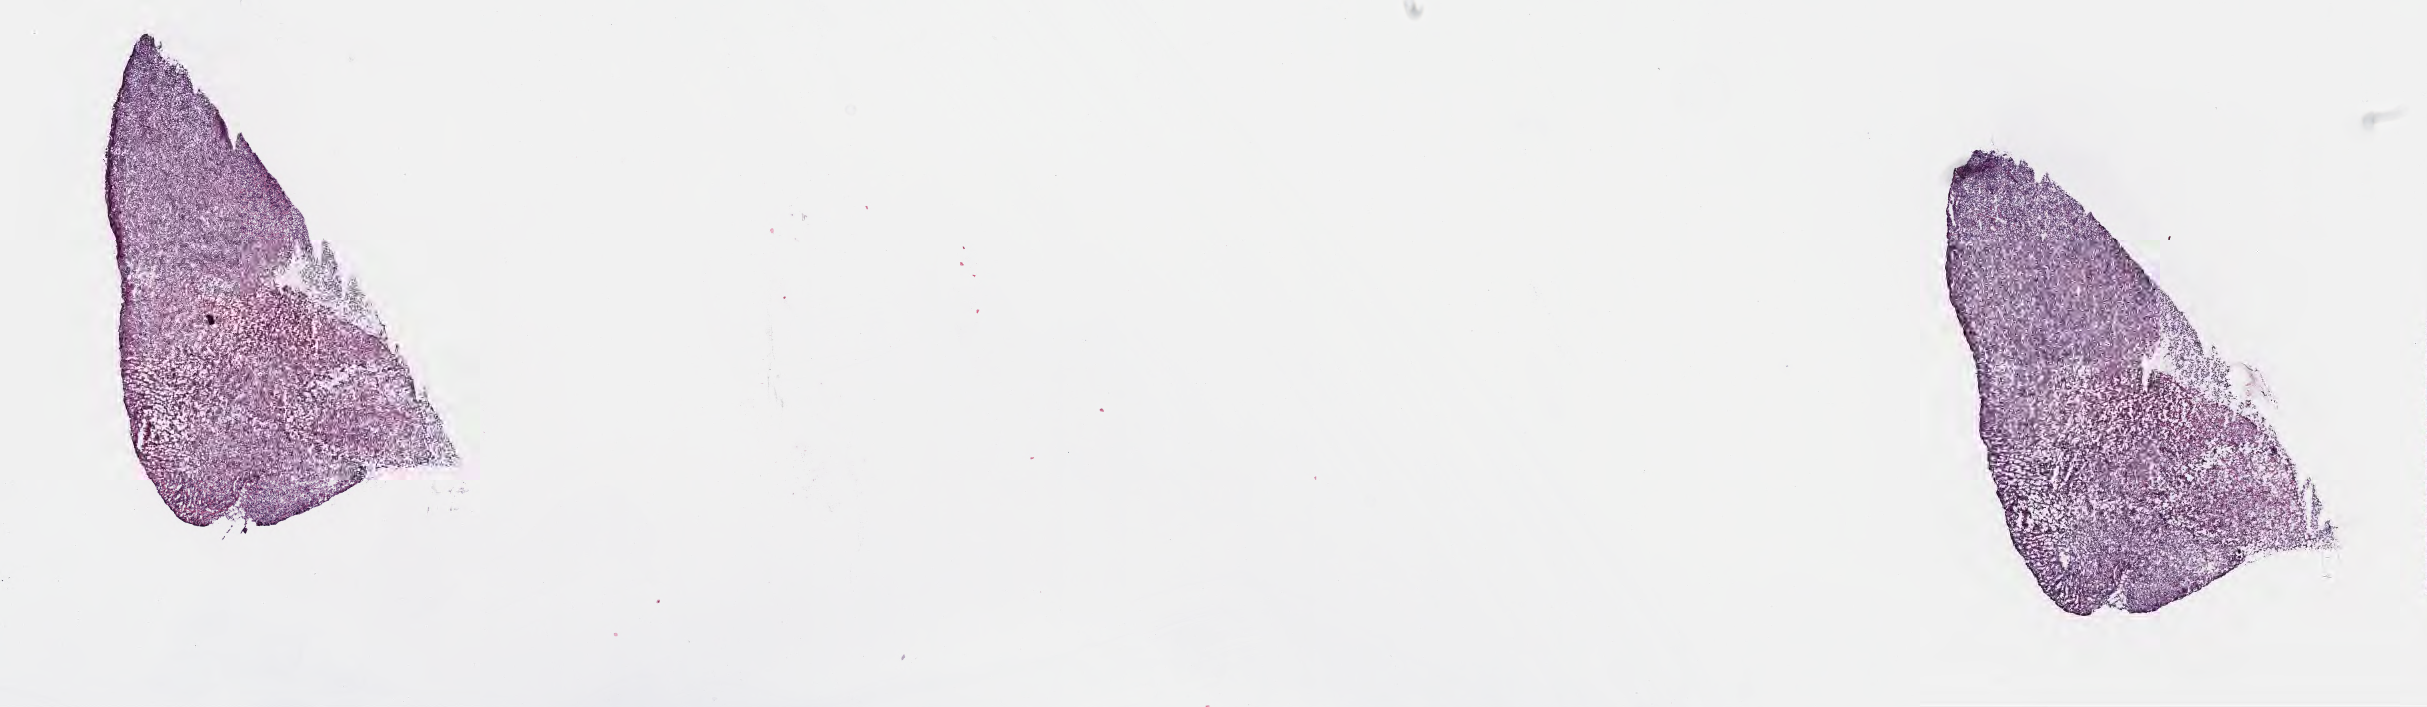
Digitized hematoxylin and eosin (H&E)-stained section, shown as a low-resolution overview of the whole scanned area (about 19.6 x 5.7 mm), cryosection, specimen: primary tumor, anatomic site: vestibule of mouth. Male, age 5 years at initial diagnosis. Composition of this section per pathologist review: tumor cells 90%, tumor nuclei 90%, stromal cells 10%, necrosis 0%, normal cells 0%. Inflammatory infiltration, as recorded: lymphocyte infiltration 70%, monocyte infiltration 20%, neutrophil infiltration 5%.
Histologic diagnosis: Diffuse large B-cell lymphoma, NOS. Section: bottom of the tissue portion. Ann Arbor stage (patient): Stage IV.